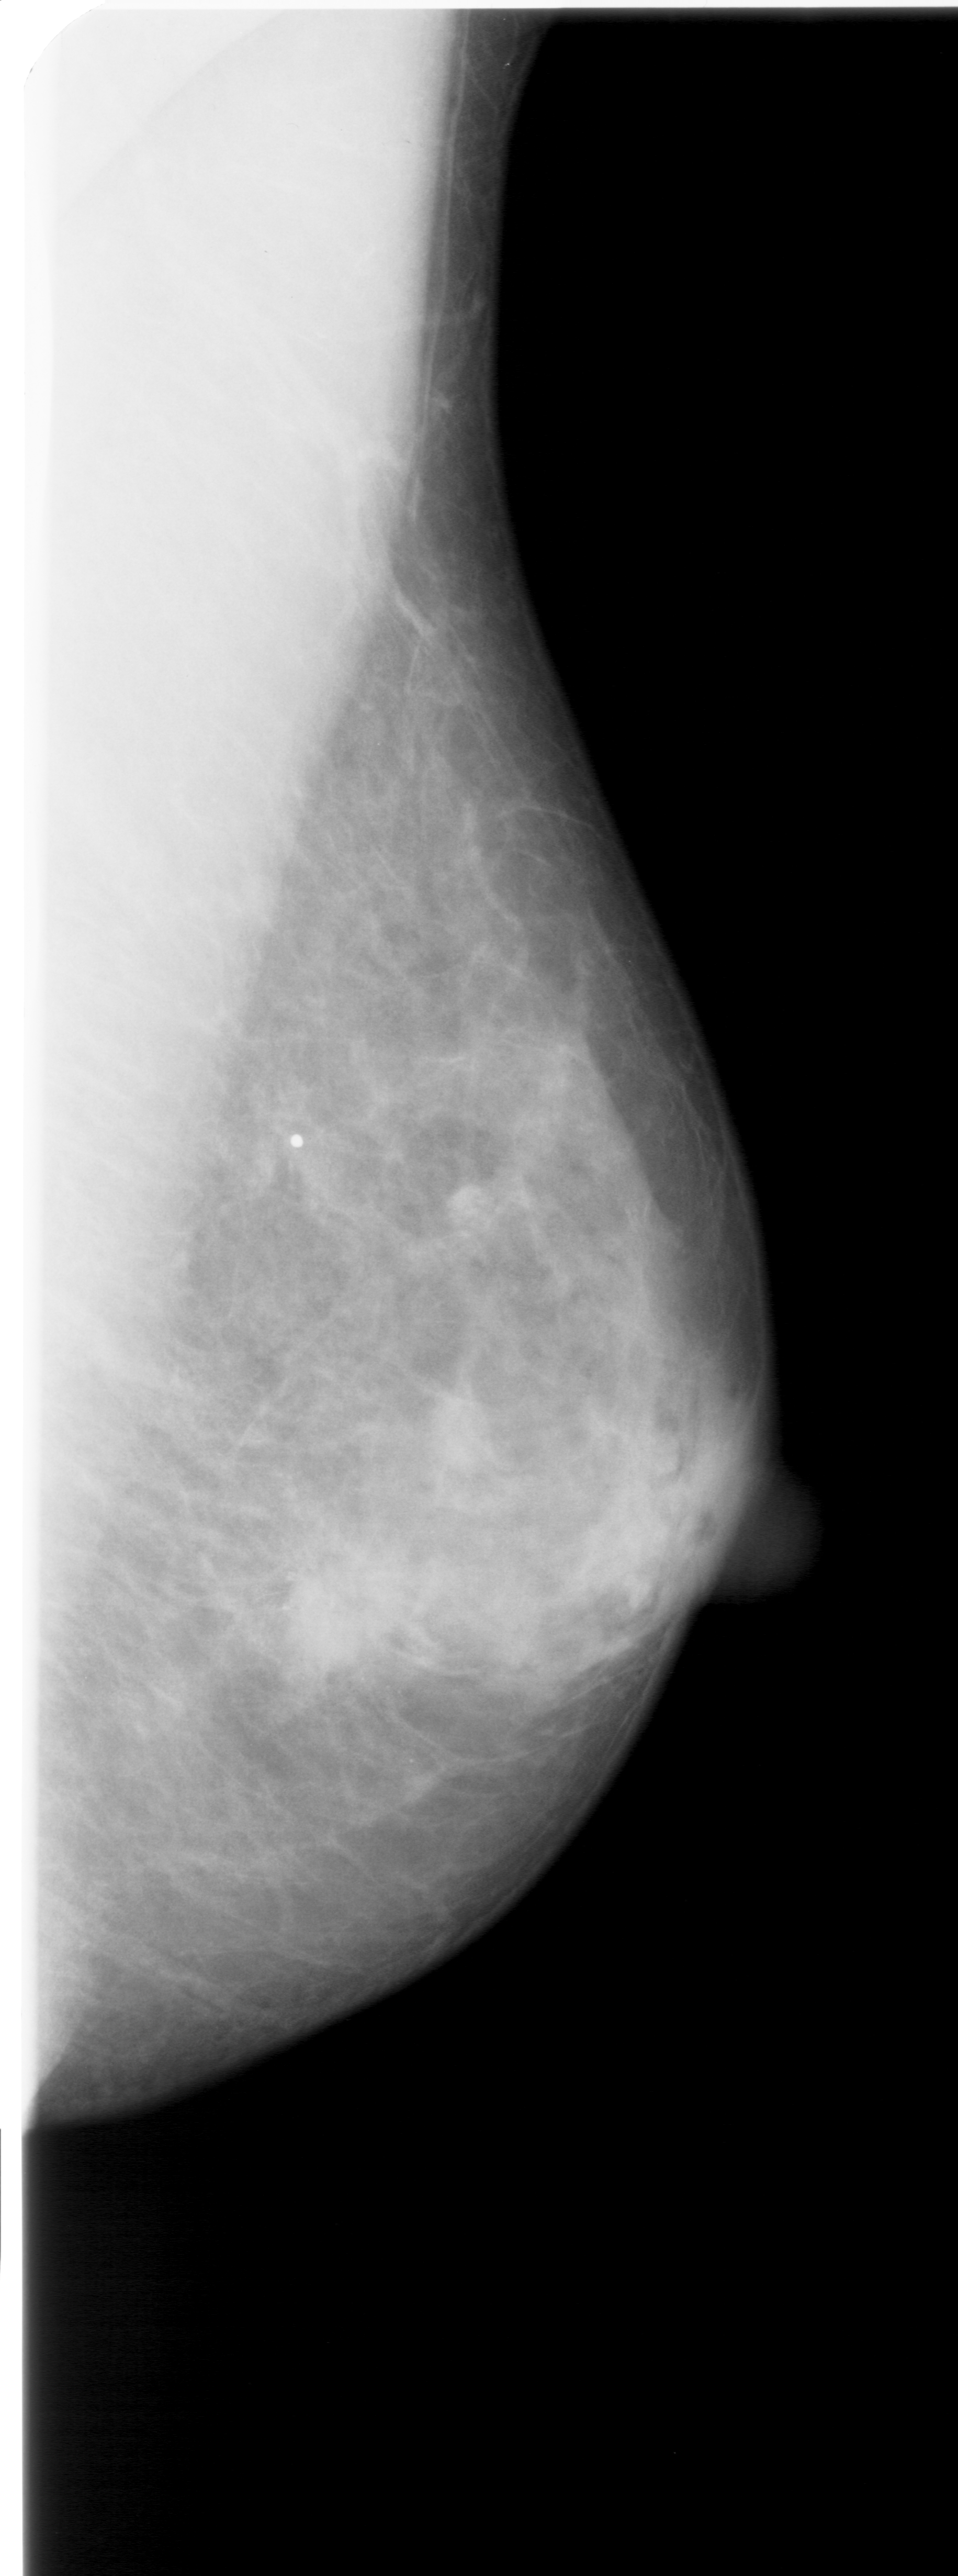
Mammogram (digitized film), right breast, mediolateral oblique (MLO) view.
- Marked findings (only marked abnormalities are described; nothing is implied about the rest of the image): calcifications, morphology pleomorphic, distribution clustered; BI-RADS assessment category 5; subtlety rating 3 on a 1 (subtle) to 5 (obvious) scale; pathology result (as recorded, not read from the image): malignant.